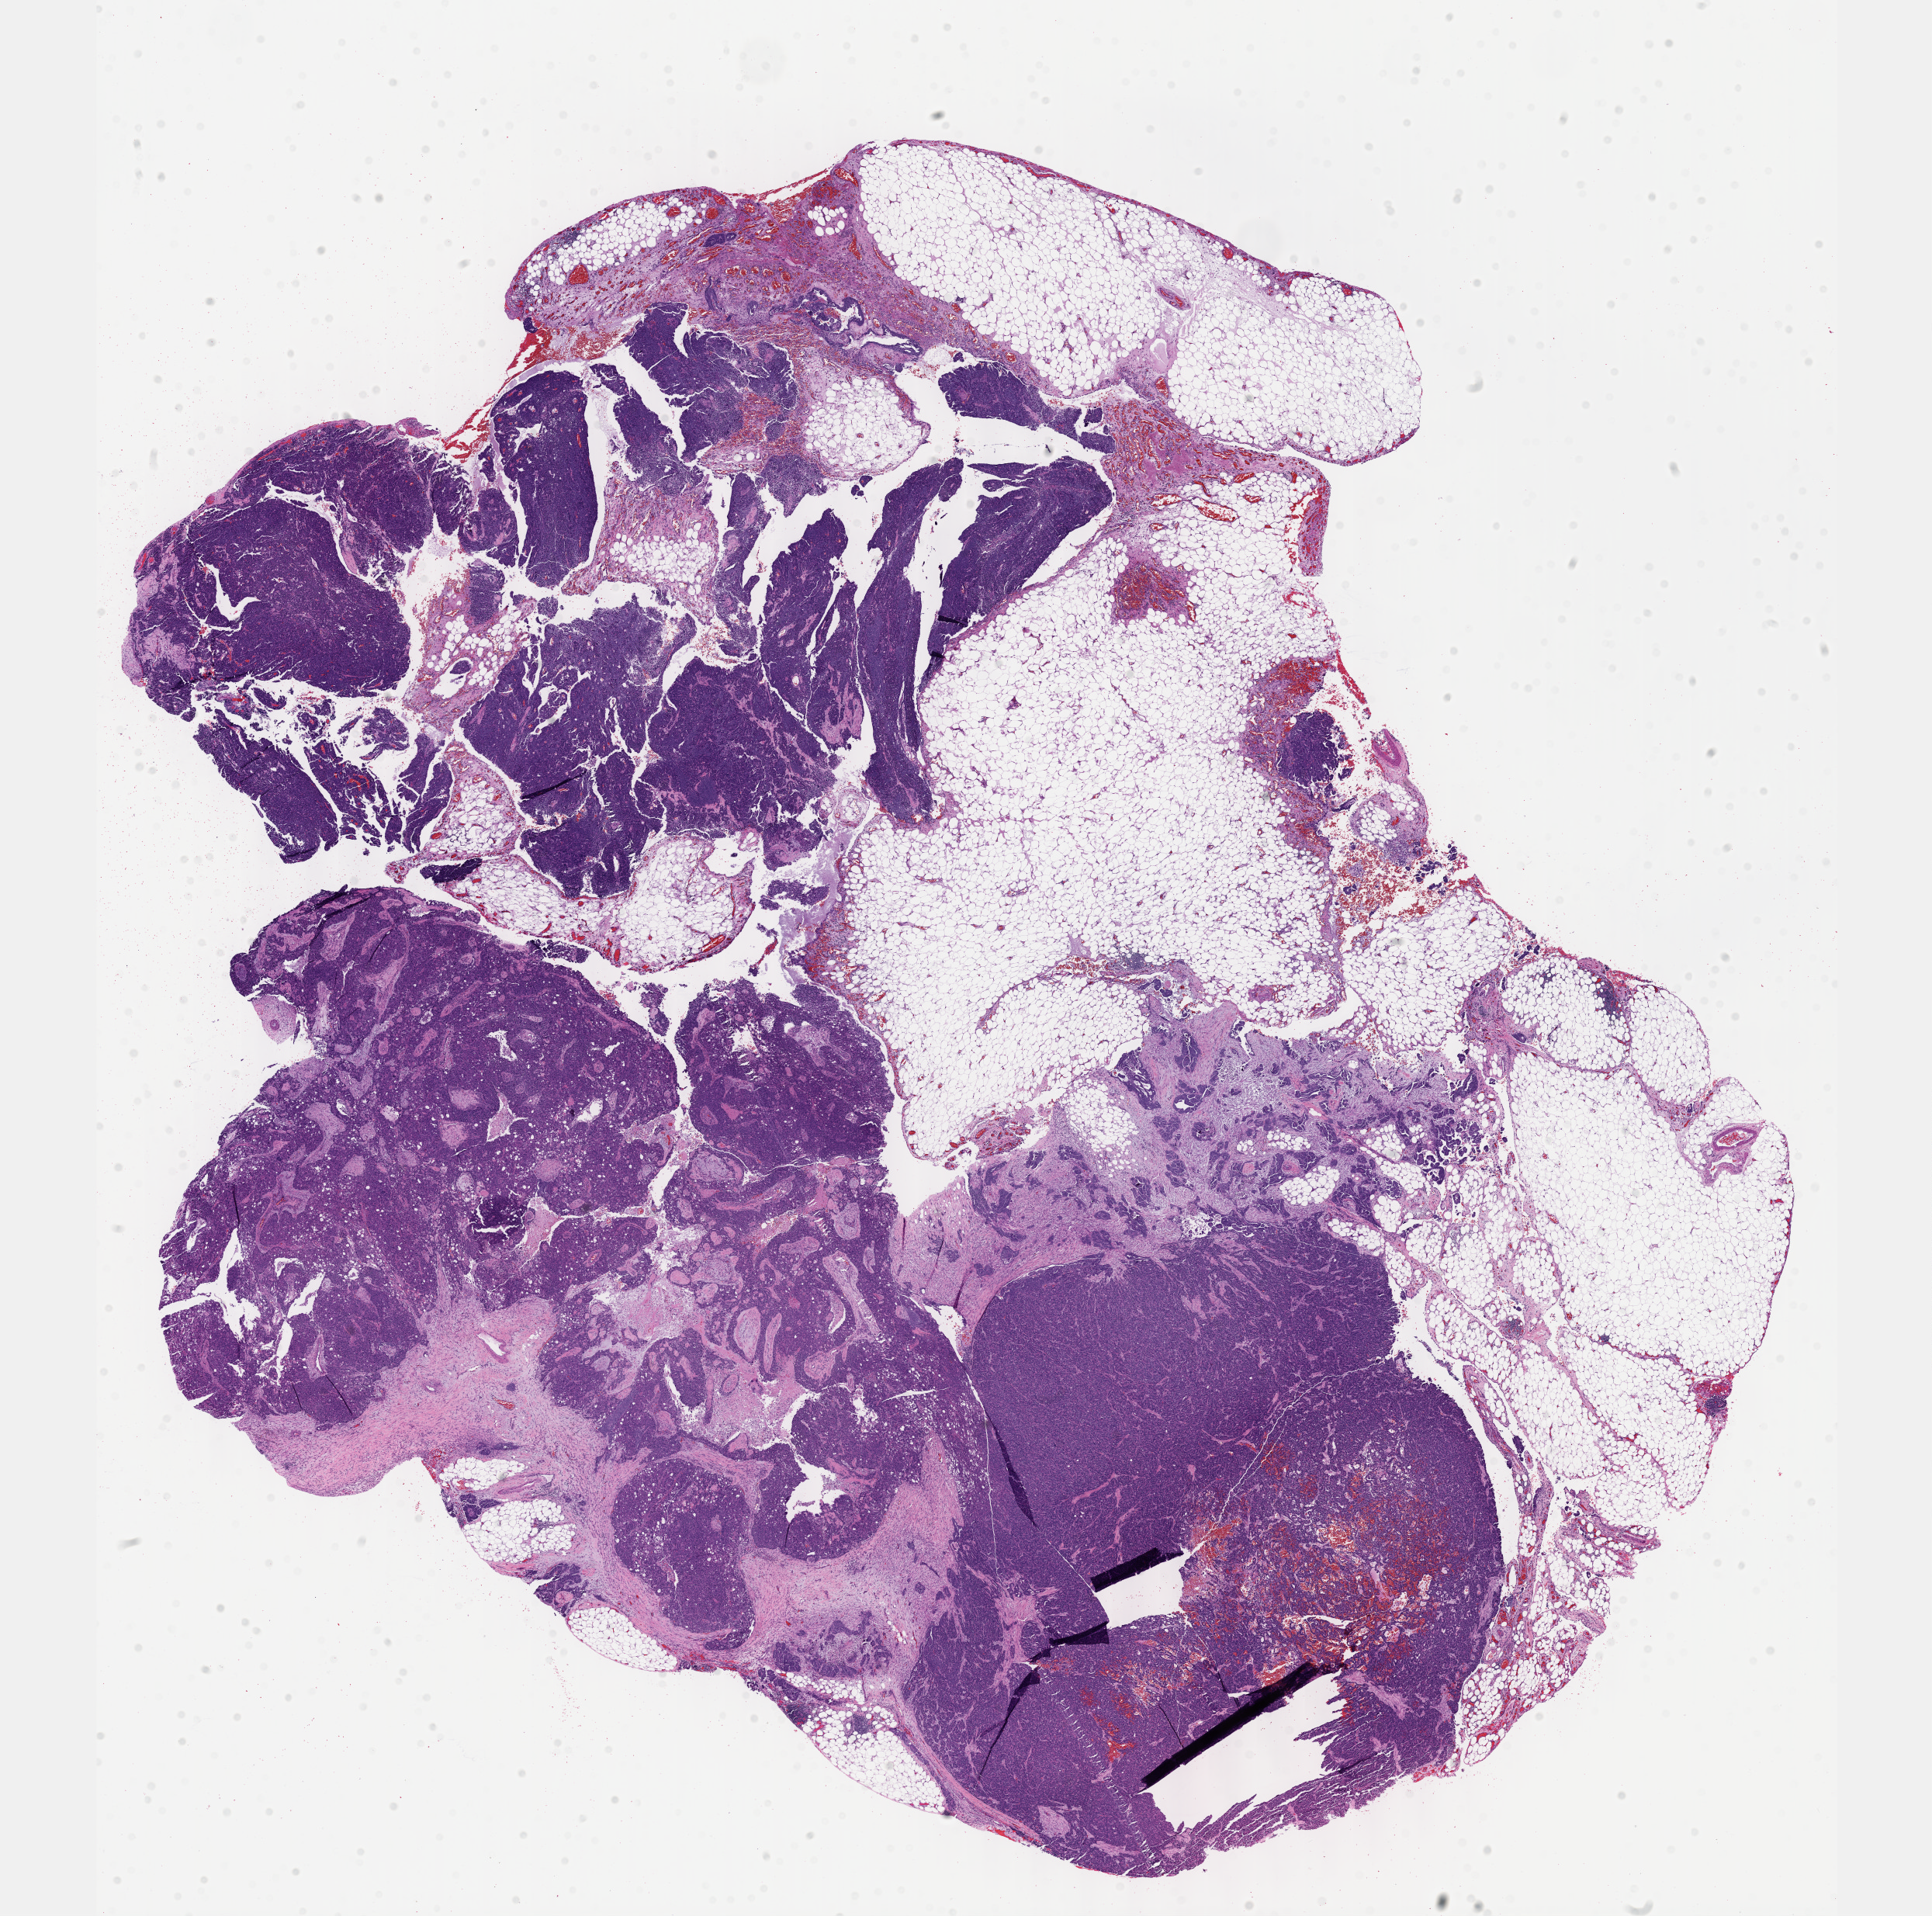
Whole-slide histology image, Hematoxylin and eosin (H&E) stained, shown as a low-resolution overview of the whole scanned area (about 20.1 x 19.9 mm, acquisition: 40x scan); formalin-fixed paraffin-embedded (FFPE) diagnostic section; ovary, primary tumour sample. Female, age 72 years at initial diagnosis. Histologic grade: G3 (poorly differentiated).
* FIGO stage: IIIC
* laterality: right
* pathologic diagnosis: Serous cystadenocarcinoma, NOS